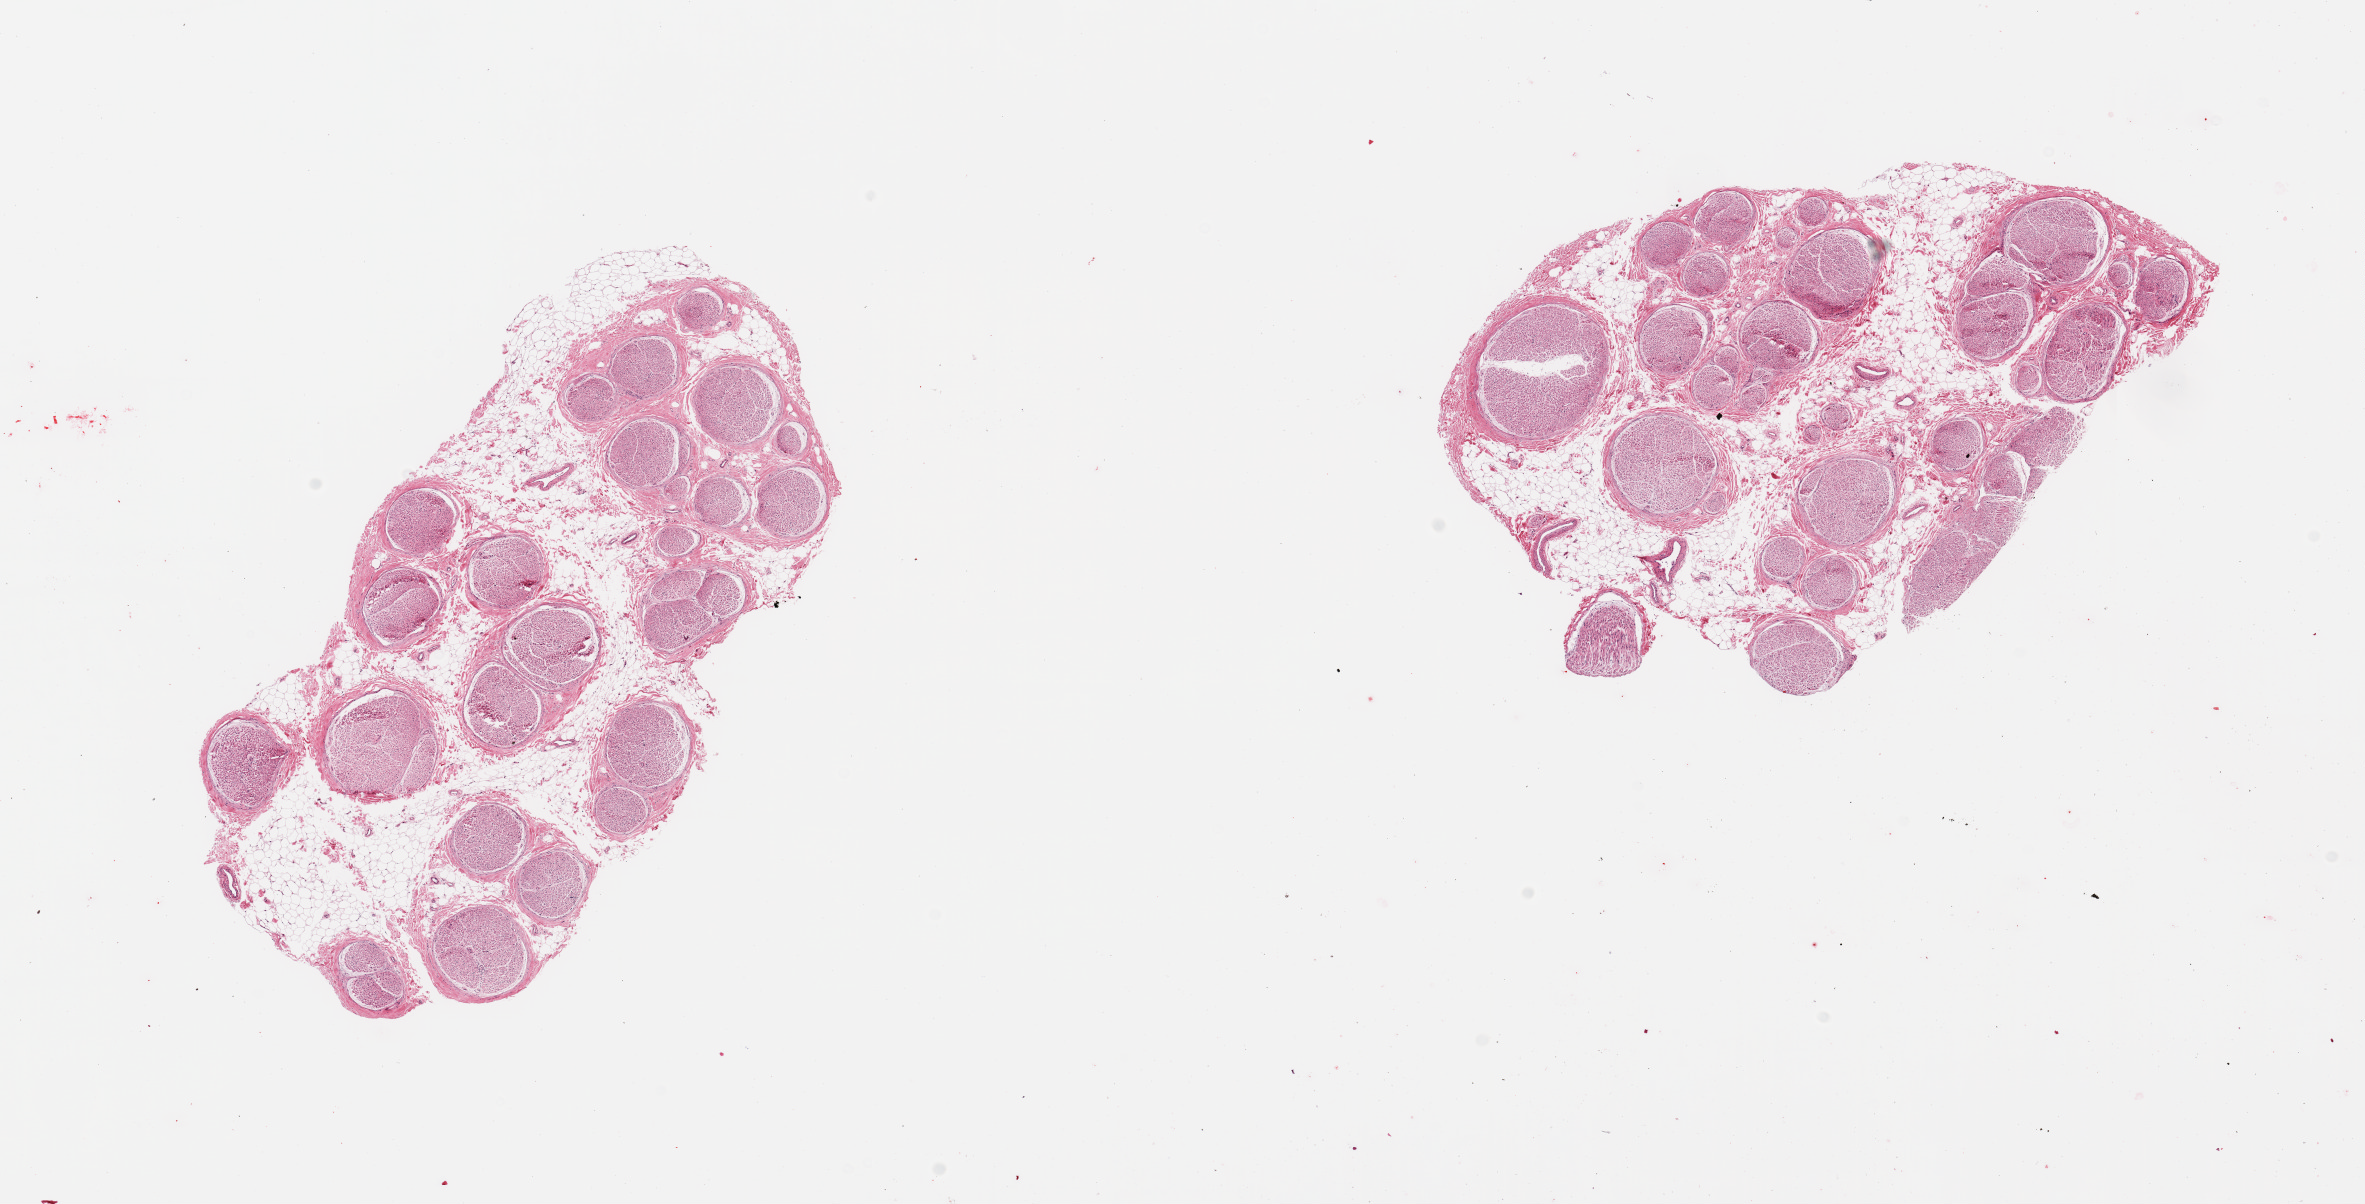
Digitized H&E-stained section — whole scanned area (about 18.7 x 9.5 mm, from a 20x scan) shown as a low-resolution overview; PAXgene-fixed, paraffin-embedded tissue; sampled site (target tissue): tibial nerve; tissue donor sample. Male donor.
- reviewer comment on this tissue sample: 2 pieces, minimal adherent fat